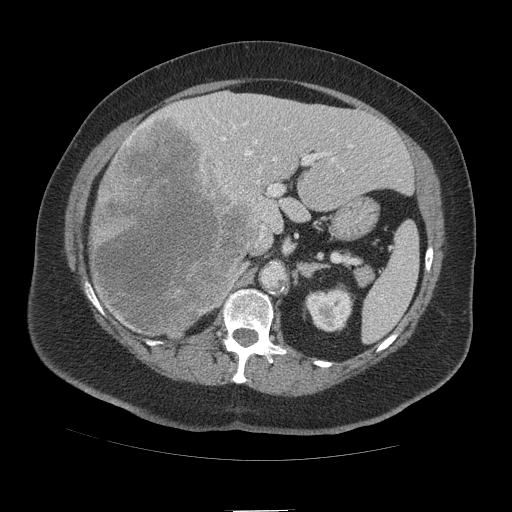
Contrast-enhanced abdominal CT (liver protocol), one axial slice; slice 61 of 109 in the series (ordered by position); 140 kVp; soft-tissue window (W 400 / L 40 HU); 2.5 mm slice thickness; 512 × 512 image matrix, field of view 420 × 420 mm. From the clinical record (not read from this slice): diagnosis: hepatocellular carcinoma (patient treated with transarterial chemoembolisation; whether this scan precedes or follows treatment is not stated here); TNM stage (as recorded): Stage-IVB; Child-Pugh class: A; tumour nodularity: multinodular.
Outlined on this slice (semi-automatic segmentation, software-assisted and operator-edited):
- liver parenchyma outside the tumour (the mass and vessels are separate outlines, so this box may not span the whole liver): bounding box <92,92,412,338> (left, top, right, bottom; pixels)
- mass: <89,114,256,338>
- liver vessels: <133,121,353,239>